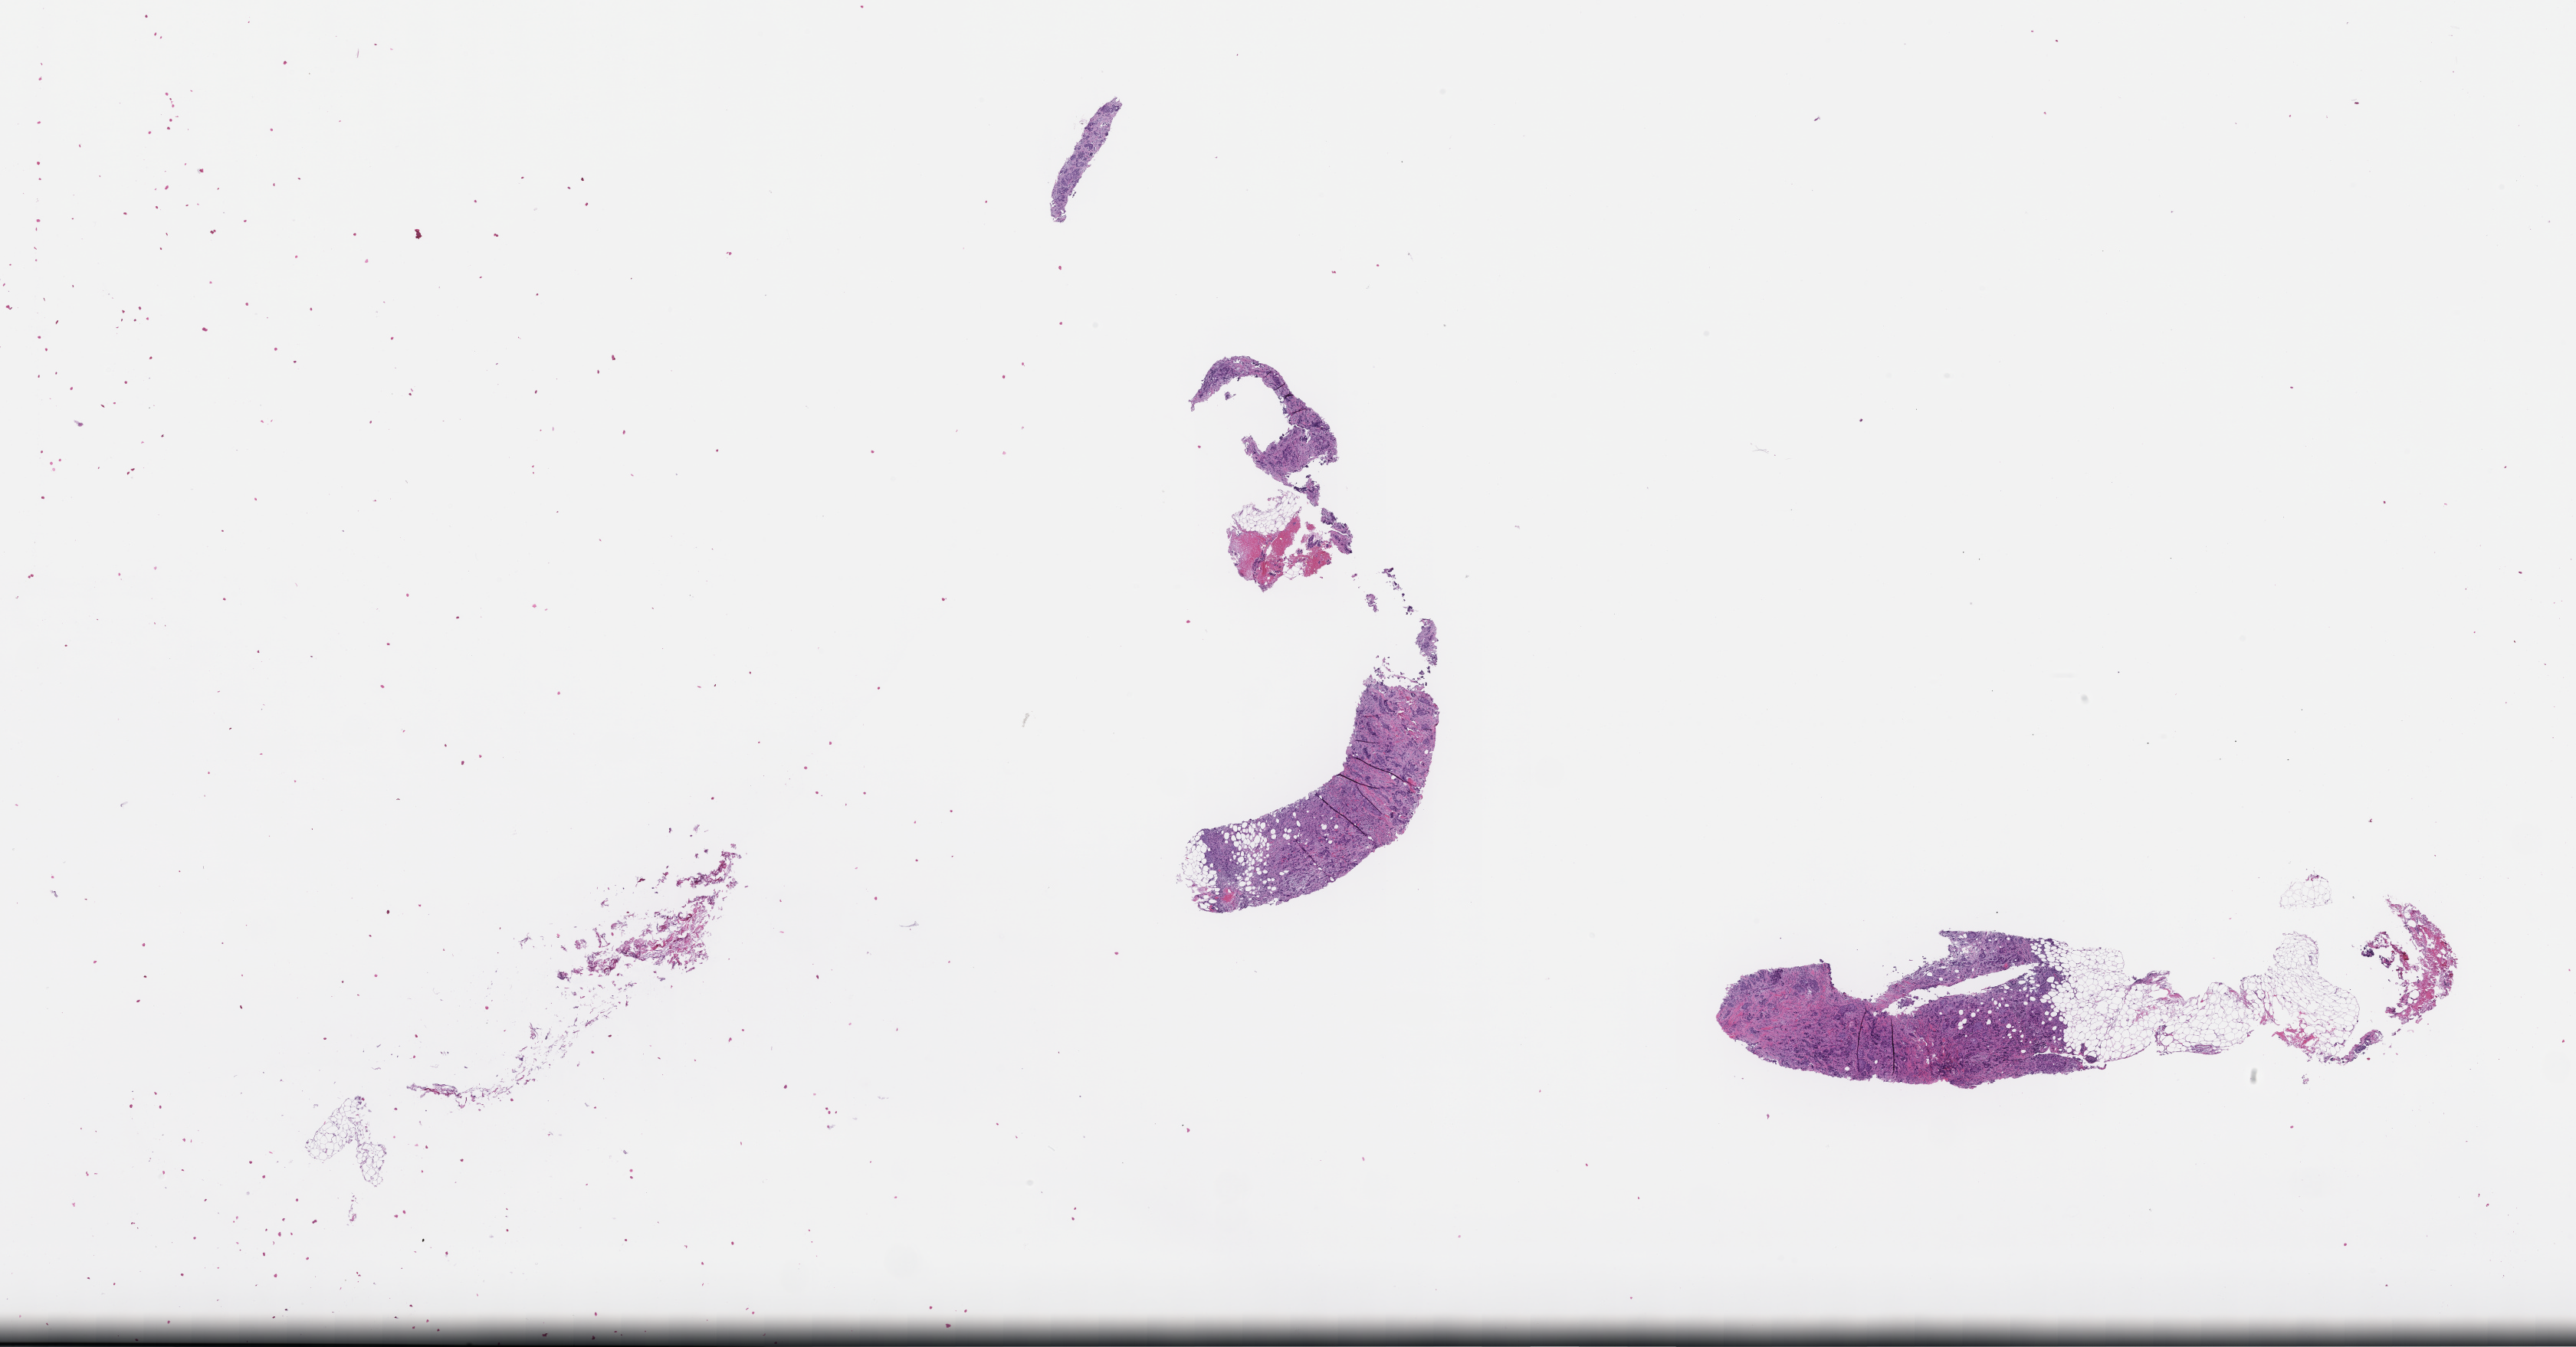
Whole-slide image, H&E stain, a low-resolution overview of the entire scanned area, about 27.1 x 14.2 mm; FFPE section; site: breast; archival tissue. Patient sex: female.
• this section: primary tumor
• diagnosis: Invasive Breast Carcinoma